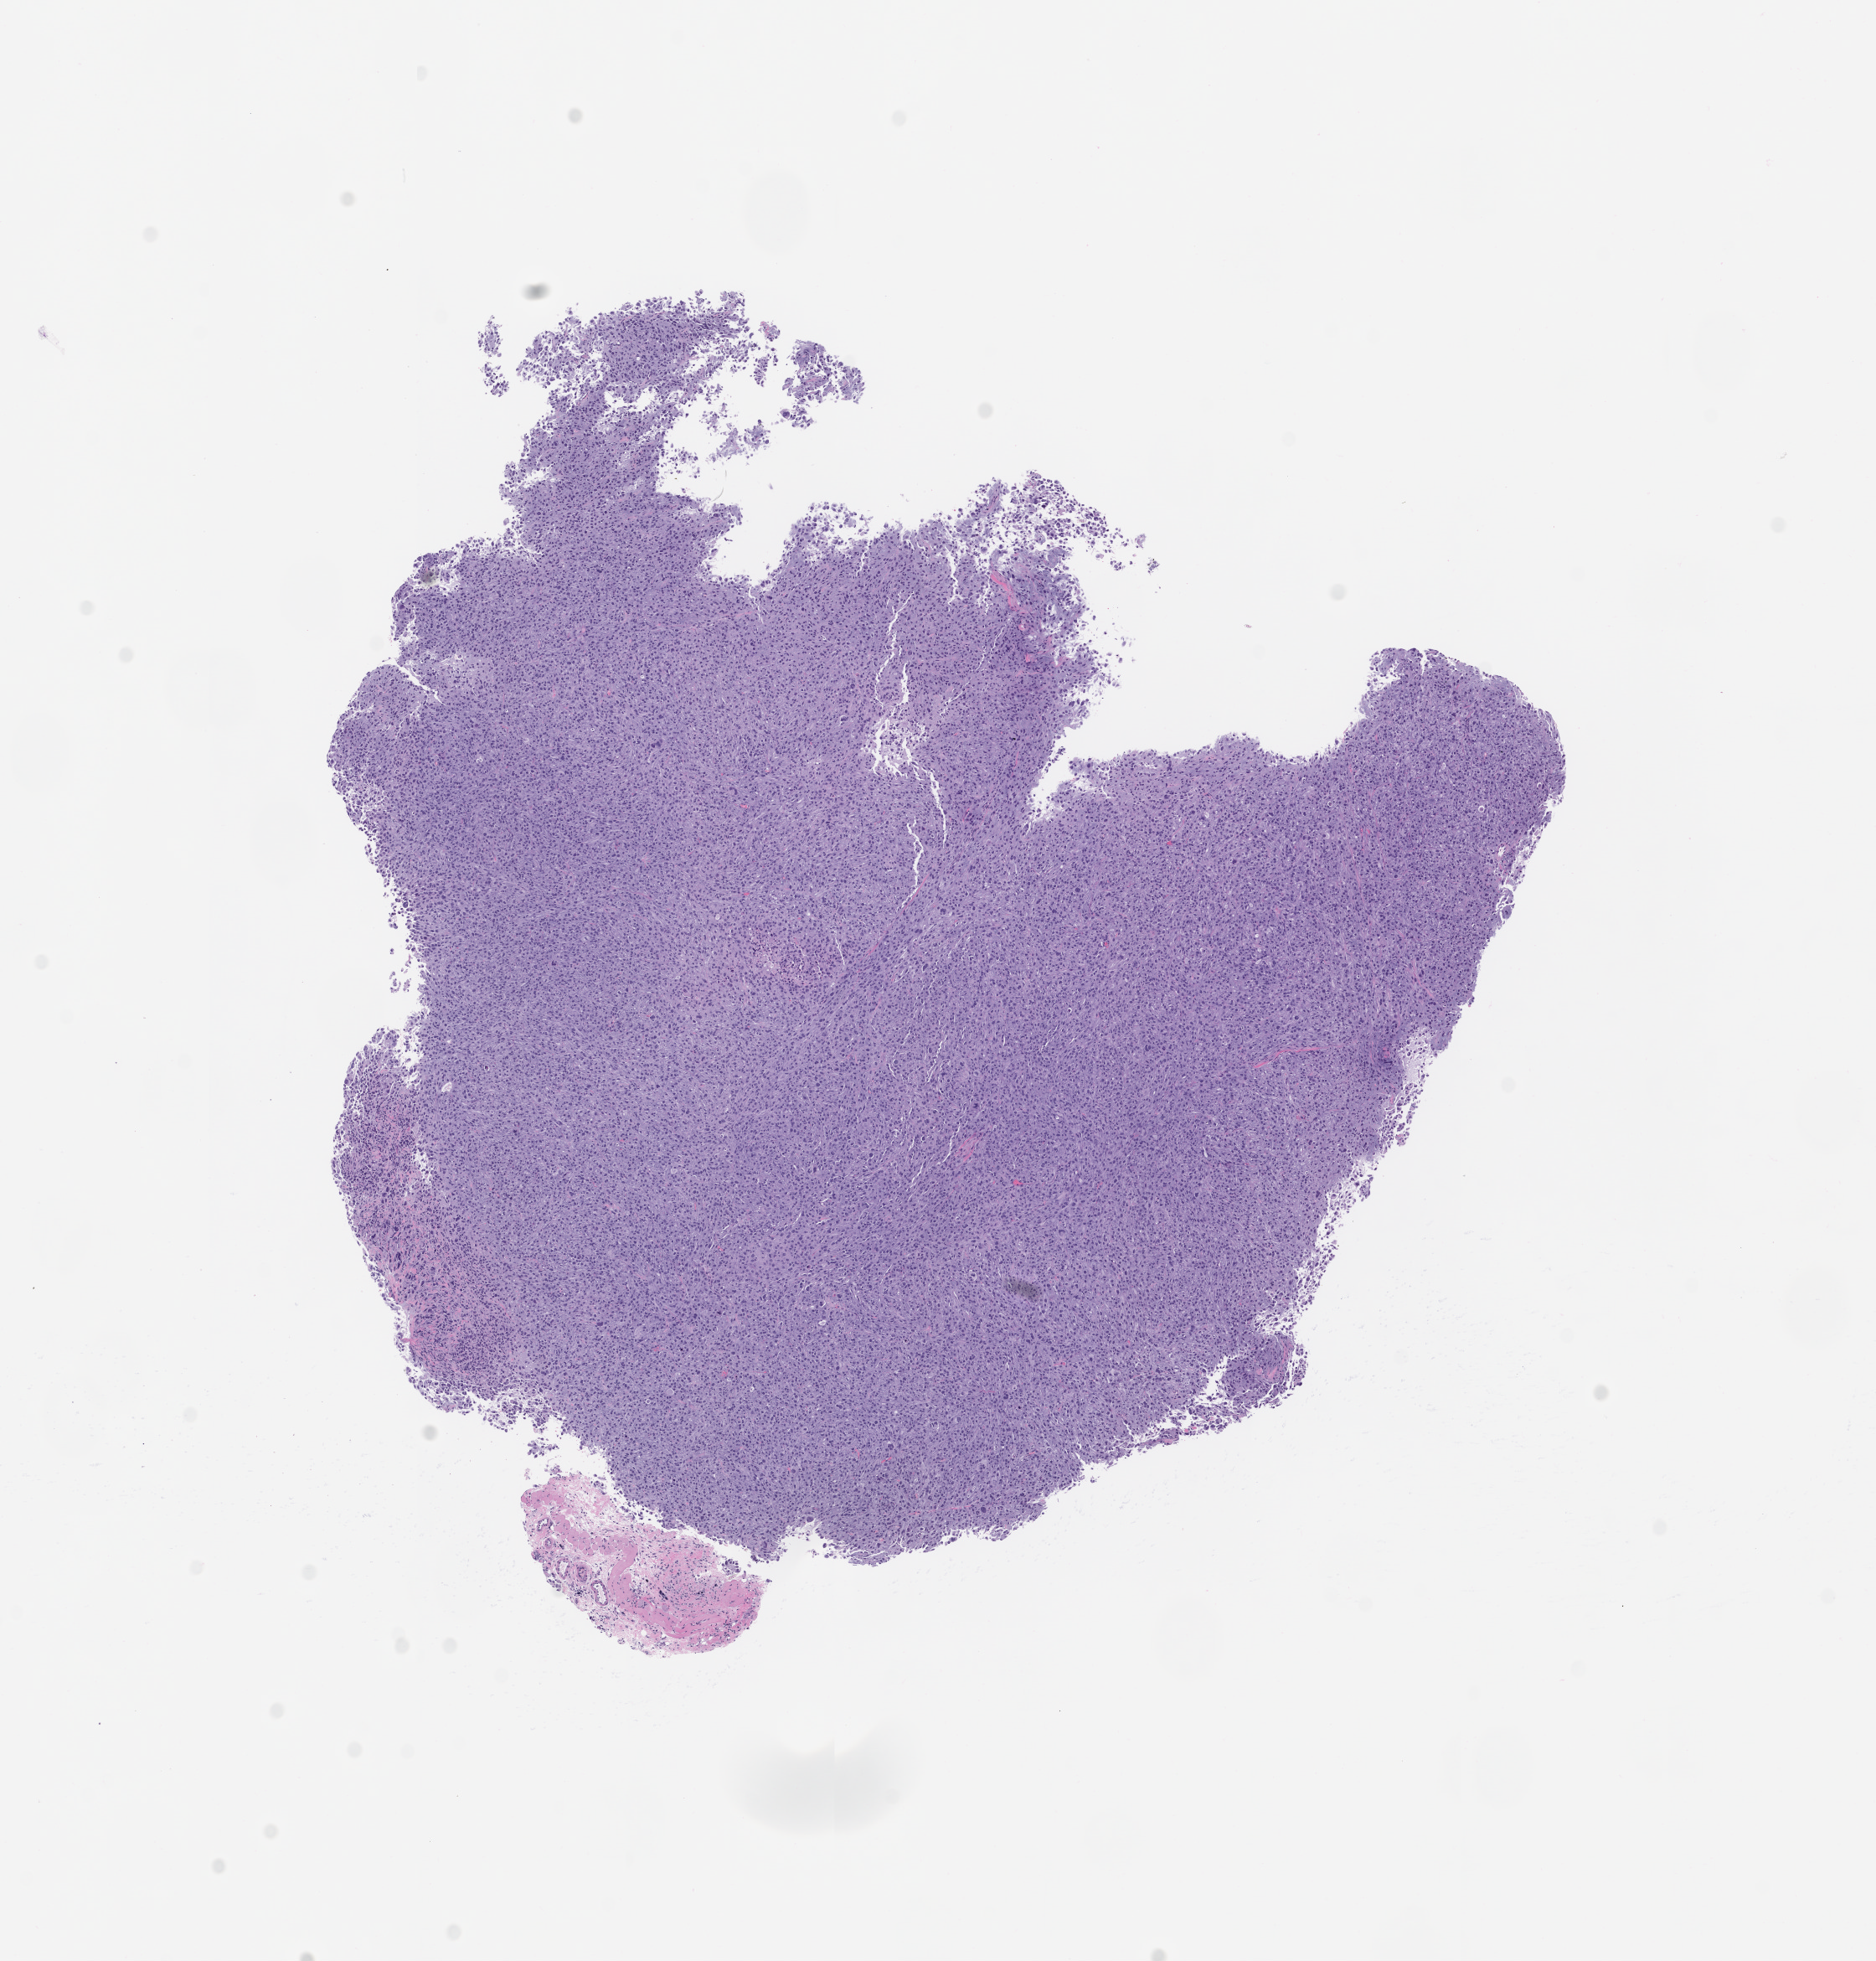
Whole-slide image, hematoxylin and eosin (H&E): patient-derived xenograft (human tumor grown in a mouse), passage 1 — whole scanned area (about 9.0 x 9.4 mm) shown as a low-resolution overview, formalin-fixed, paraffin-embedded (FFPE) tissue, originating tumor site category: thyroid.
* originating patient diagnosis: Thyroid Gland Oncocytic Carcinoma